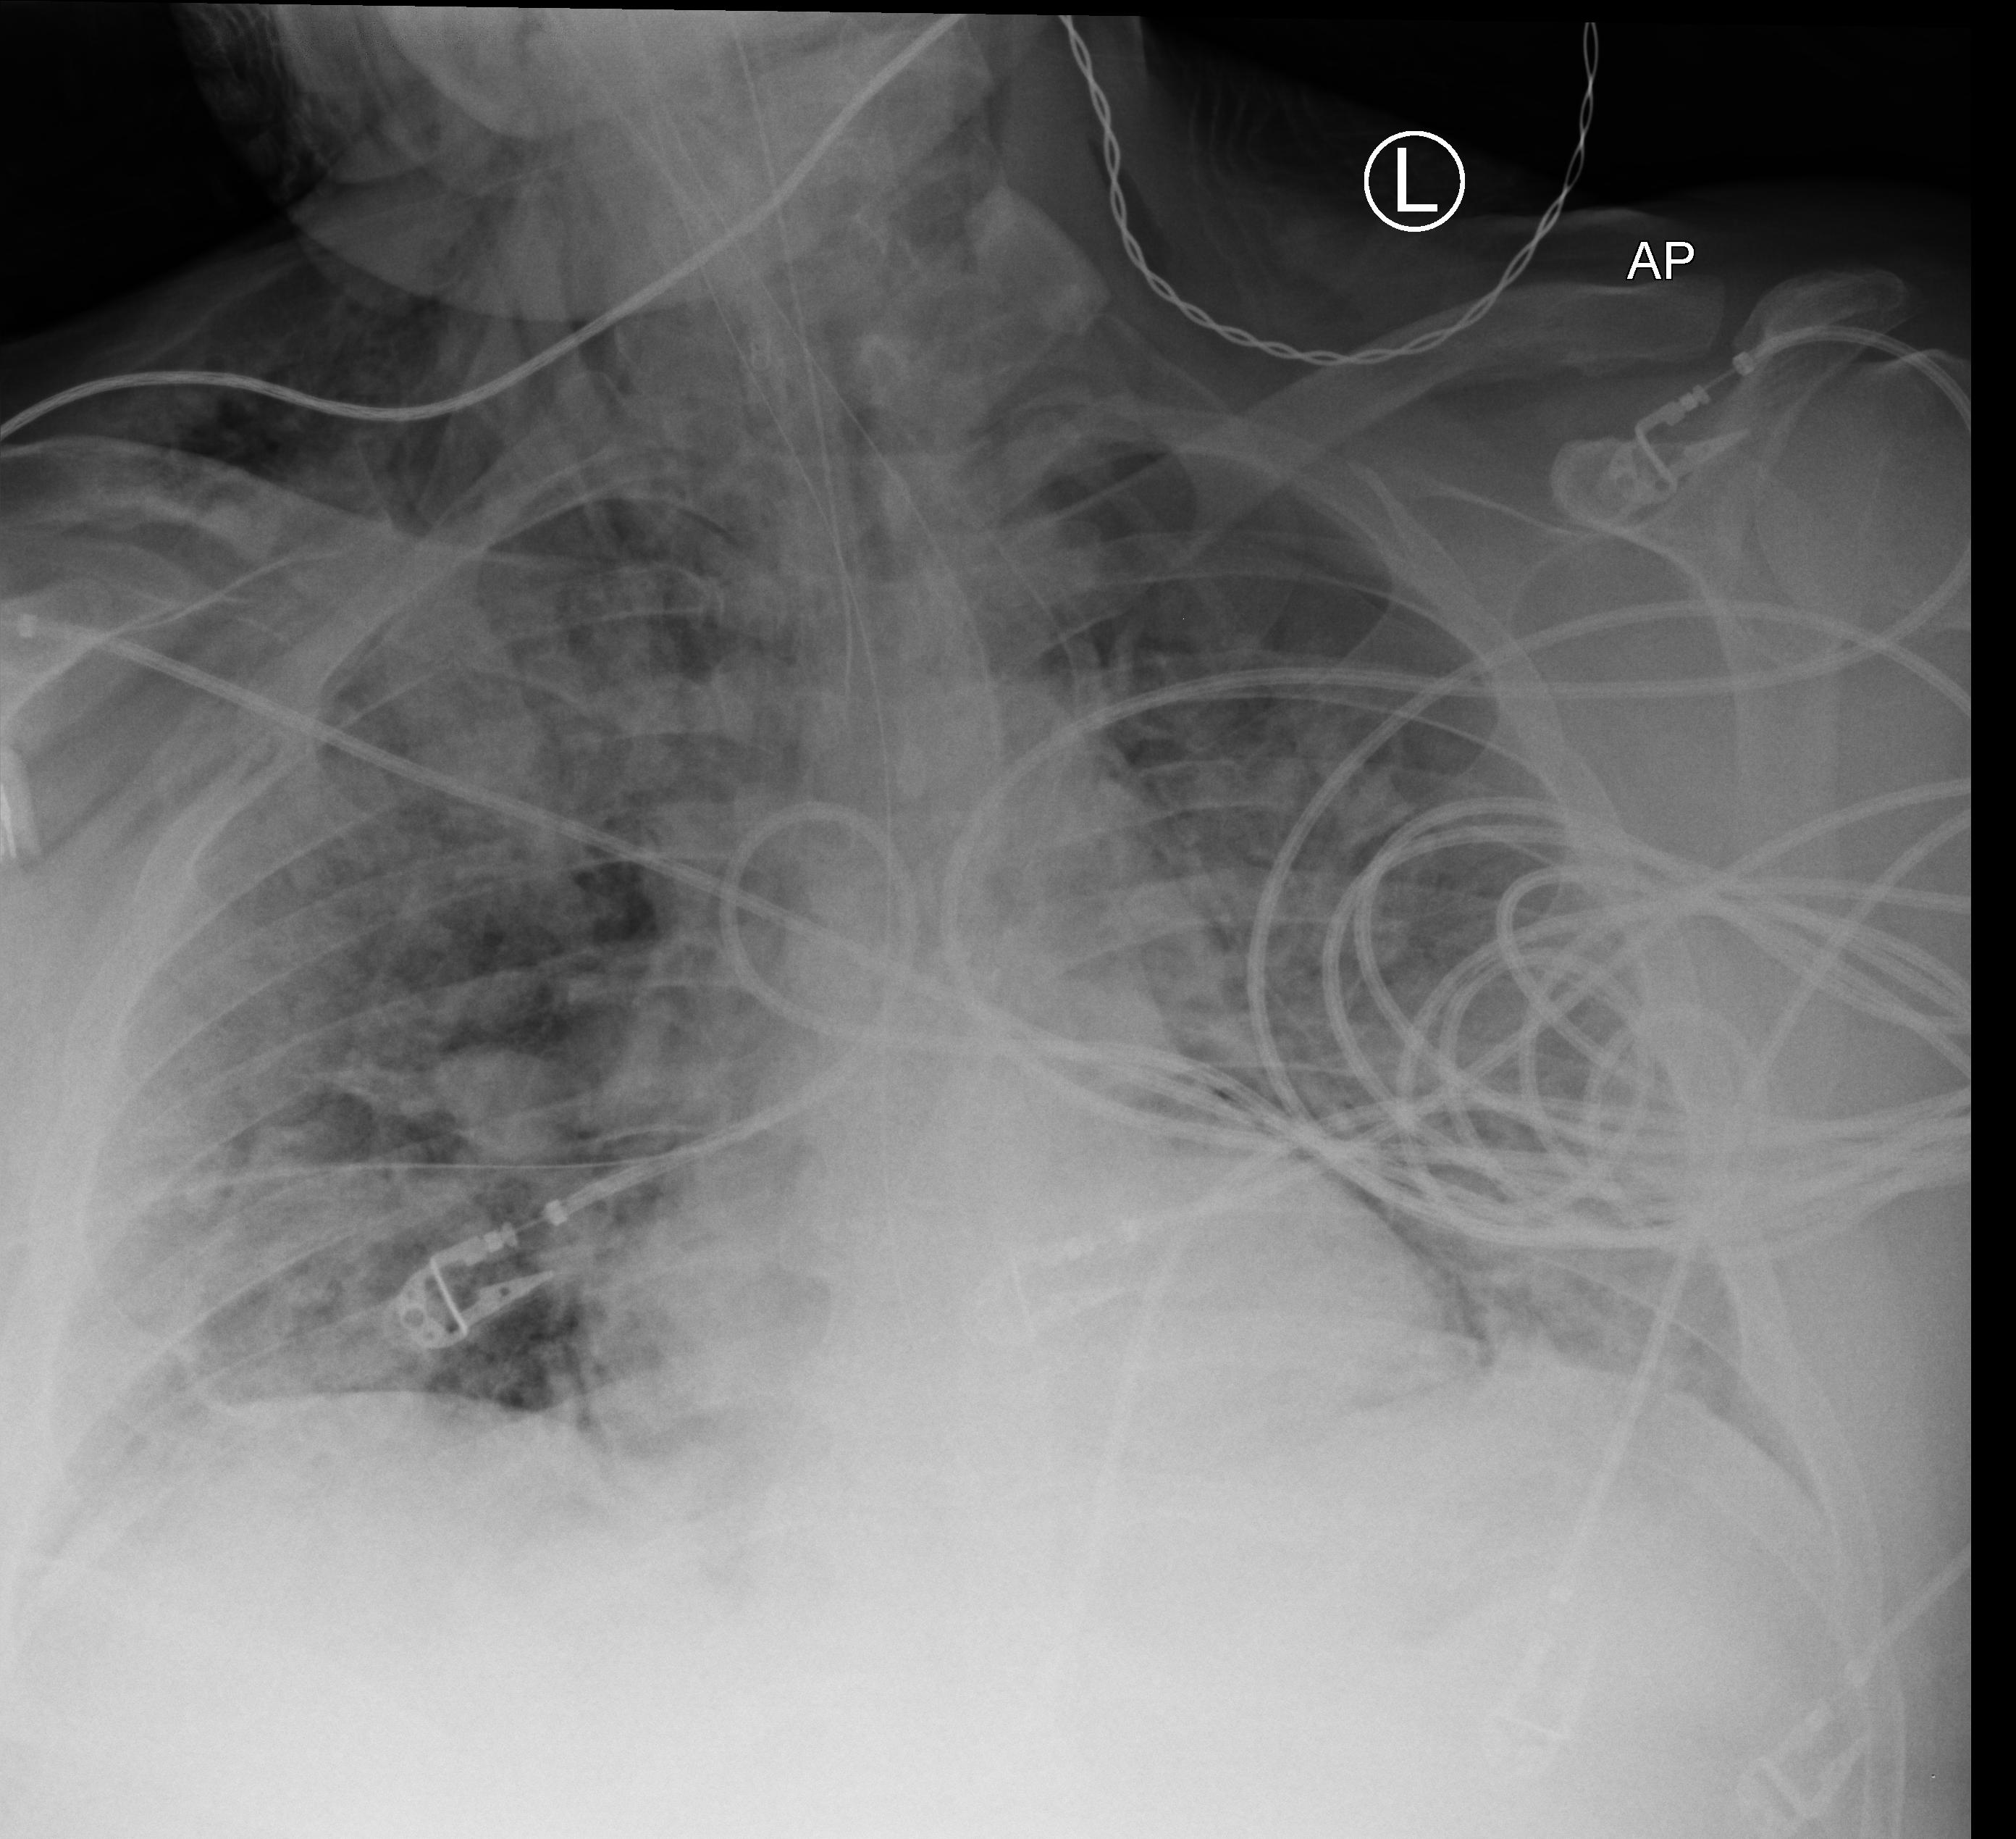
Bedside chest radiograph (computed radiography); anteroposterior (AP) projection. Adult patient hospitalised with COVID-19, age 18–59 years.
From the hospital-stay record, not from the radiograph (when in the stay this image was taken is not recorded): admitted to intensive care during this hospital stay: yes.